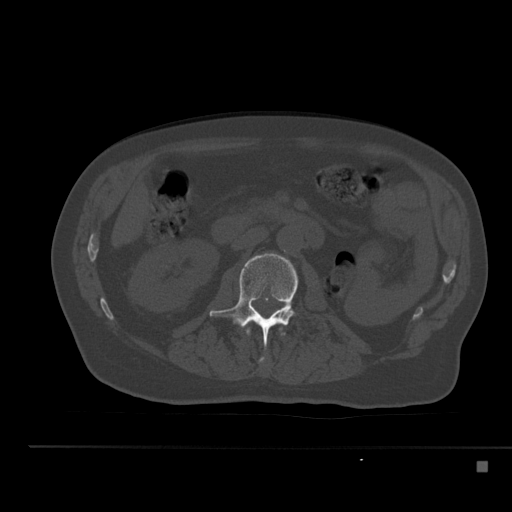
CT including the spine, one axial slice. Slice 186 of 517 in the series (ordered by position). 120 kVp. Bone window (W 1800 / L 400 HU). 1.5 mm slice thickness. 512 × 512 image matrix. Male patient, age 70 years. From the clinical record (not read from this slice): primary cancer: renal; vertebrae with lytic lesions (as recorded): T4, T6, T10, T12, L3, L4, L5.
Annotated regions visible in this slice (semi-automatic segmentation, software-assisted and operator-edited):
- L1 vertebra: bounding box [x1, y1, x2, y2] px = [246, 327, 285, 363]
- L2 vertebra: [209, 253, 298, 348]